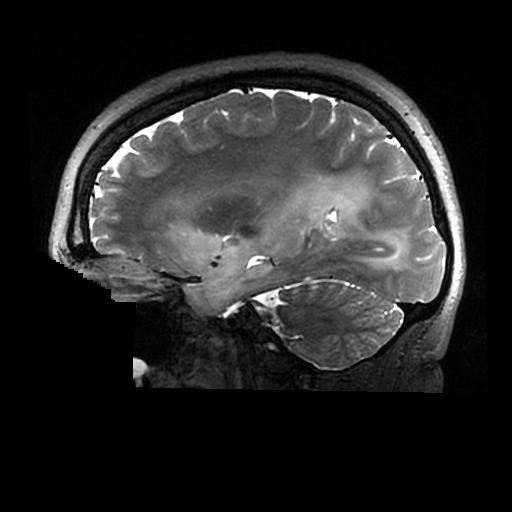
Brain MRI from a brain-tumour surgery series, one sagittal slice; position 188 of 320 along the scan axis; 512 × 512 image matrix, field of view 240 × 240 mm. From the clinical record (not read from this slice): histopathology: Astrocytoma; WHO grade: 2; IDH mutation: yes.
Structures marked on this image (outlined manually by an expert reader):
- tumour: bounding box (x1, y1, x2, y2) in pixels: (173, 183, 407, 311)